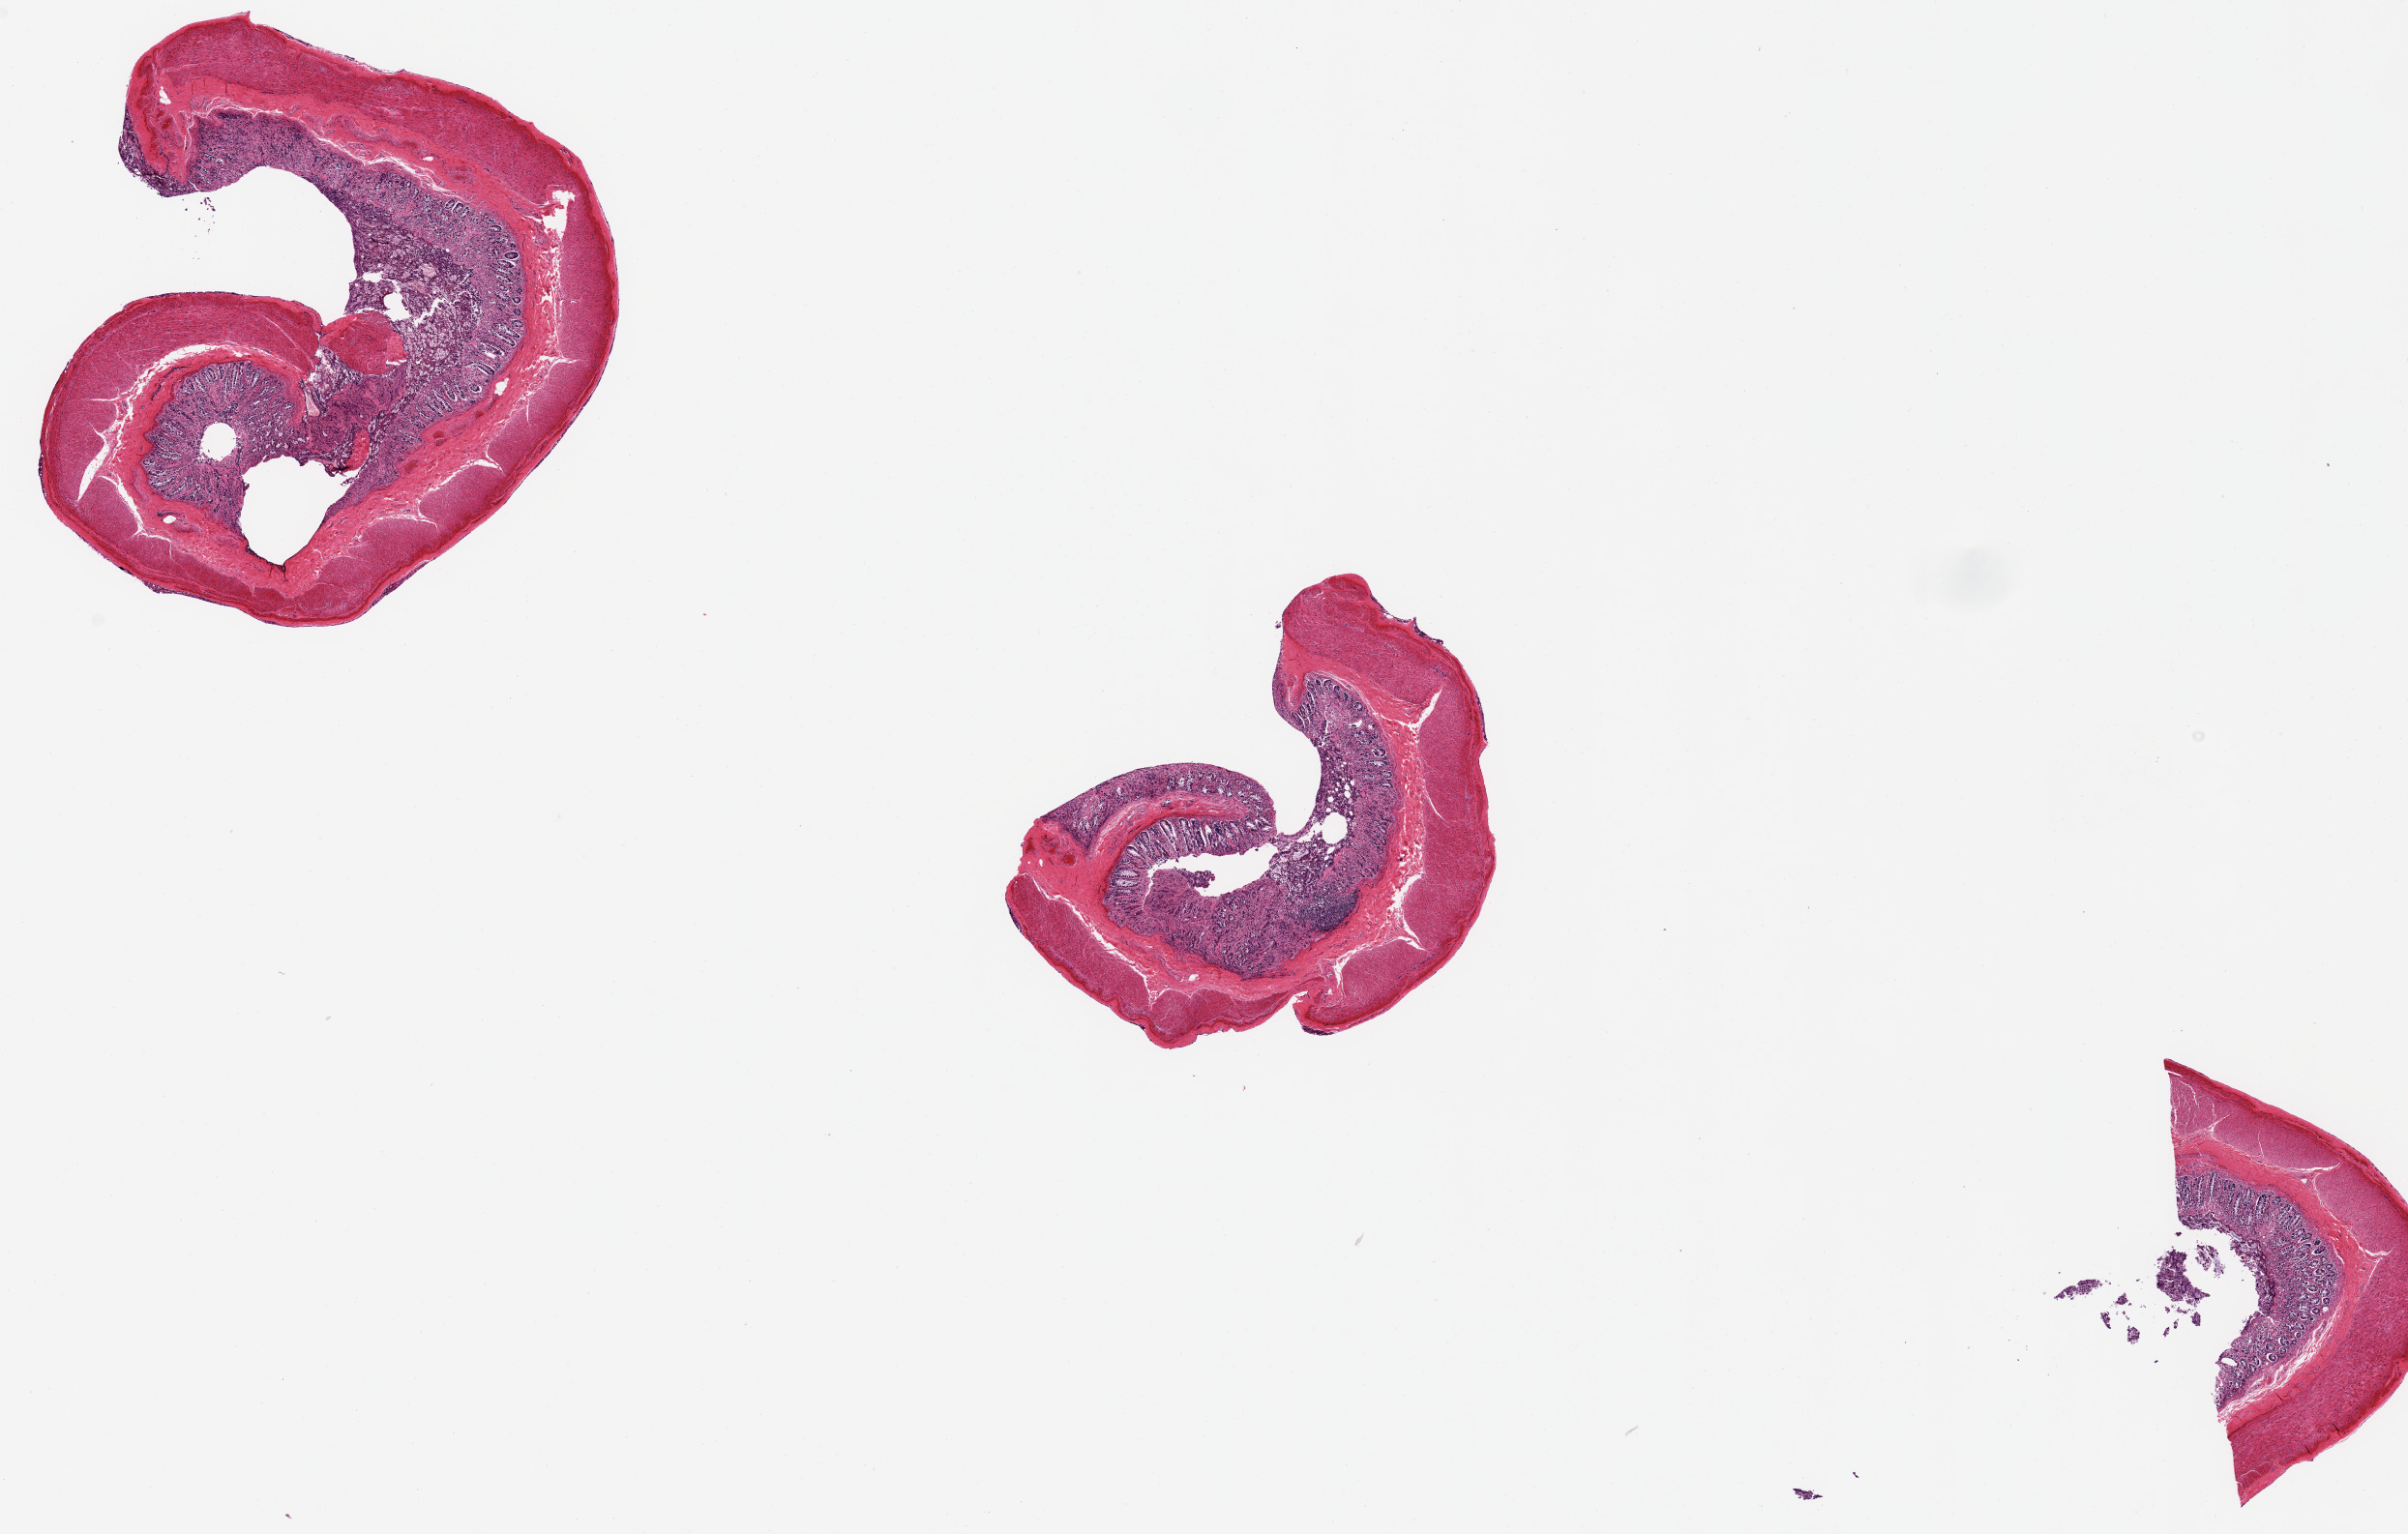
H&E whole-slide image, brightfield, shown as a low-resolution overview of the whole scanned area (about 19.7 x 12.5 mm), PAXgene-fixed, paraffin-embedded tissue, target tissue: transverse colon, donor tissue sample. Donor sex: male.
Pathologist's review note for this sample: considerable glandular autolysis.